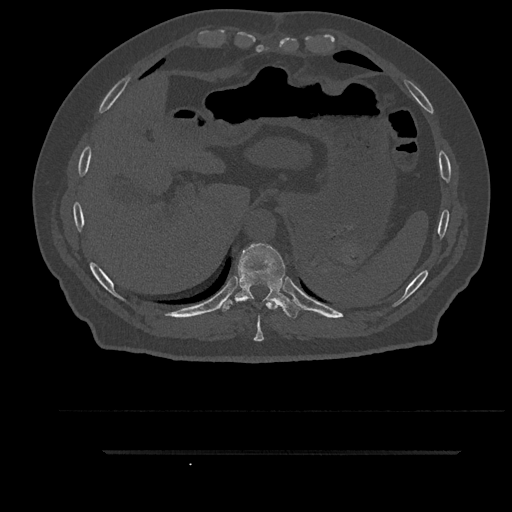
CT including the spine, one axial slice. Position 388 of 797 along the scan axis. 120 kVp. Bone window (W 1800 / L 400 HU). 512 × 512 image matrix, field of view 432 × 432 mm. Male patient, age 63 years. Case-level facts recorded for this patient, not image findings: primary cancer: renal; vertebrae with lytic lesions (as recorded): T8.
Structures marked on this image (semi-automatically segmented with operator editing):
- T10 vertebra: bounding box <221,243,302,318> (left, top, right, bottom; pixels)
- T9 vertebra: <254,300,278,342>